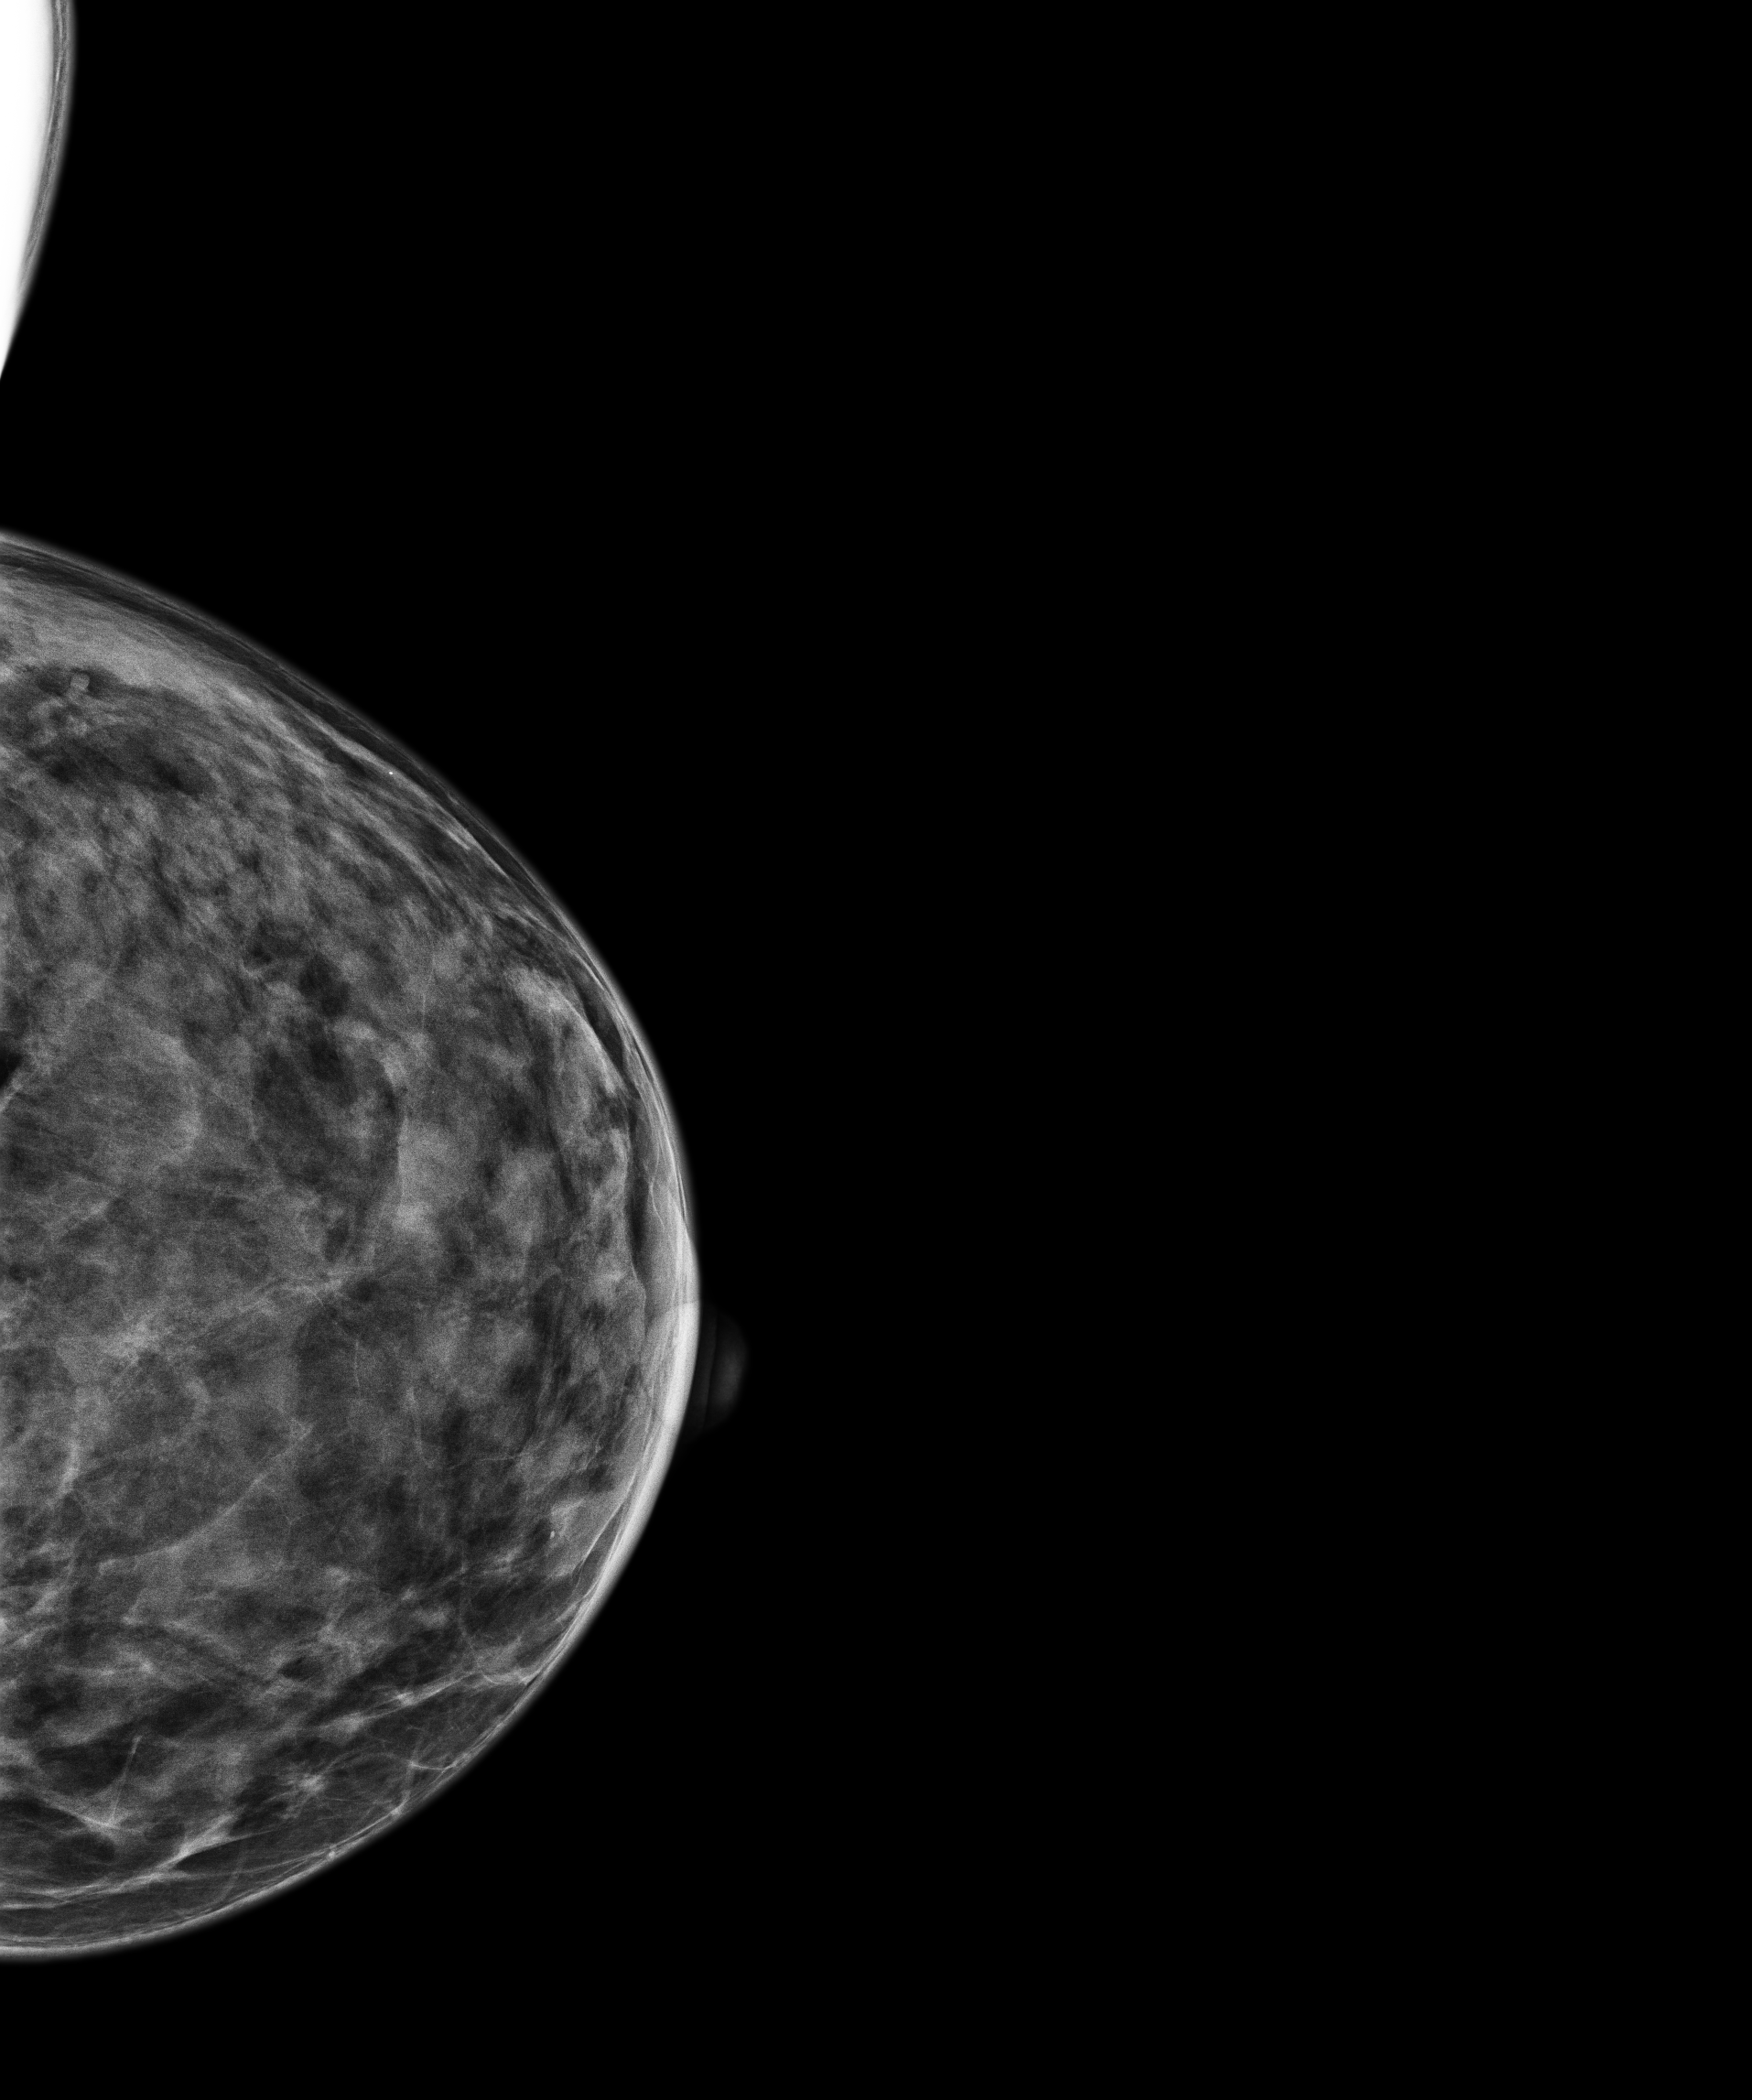
Annual screening mammography examination, compressed breast thickness 30.6 mm, system: Senographe Pristina. Female patient, age 46 years.
Image type: full-field digital mammogram. Breast: left. Projection: CC view.